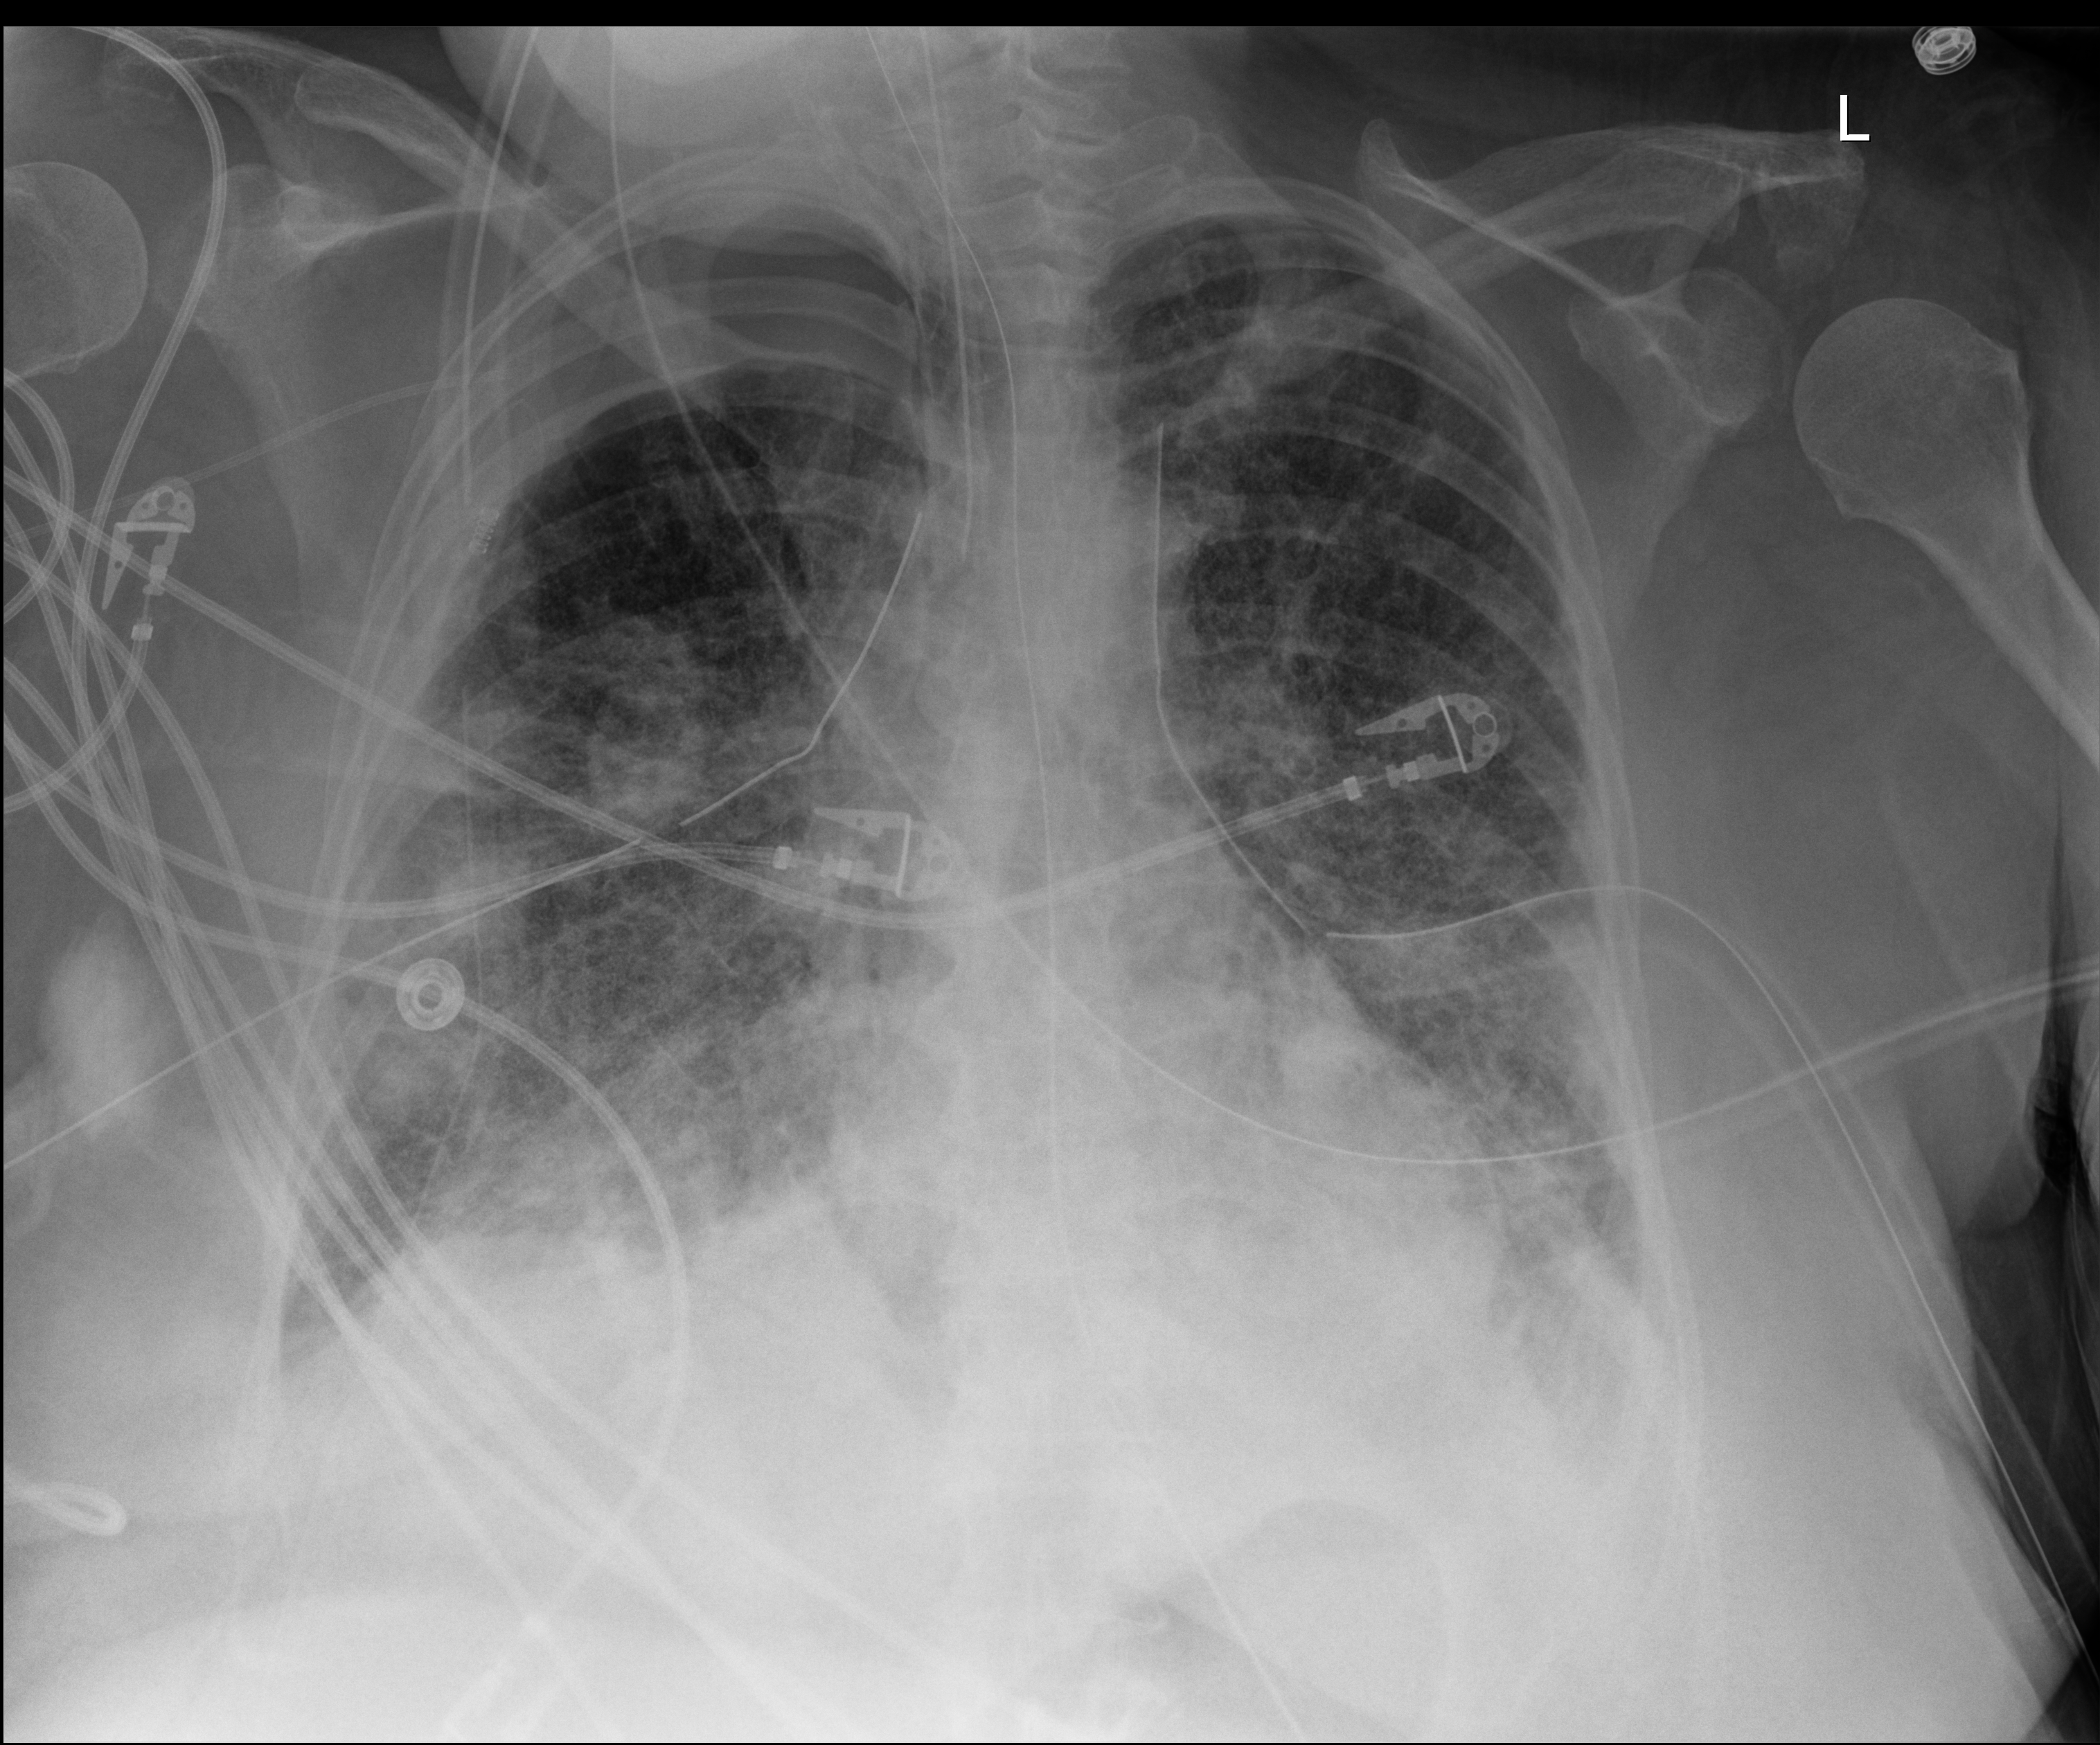
Bedside chest radiograph (digital radiography); anteroposterior (AP) projection. Patient hospitalised with COVID-19; female, aged 60–74 years.
Admission-level facts for this patient (not findings on this image; timing relative to this image not recorded):
- length of hospital stay: 38 days
- chronic kidney disease (admission record): no